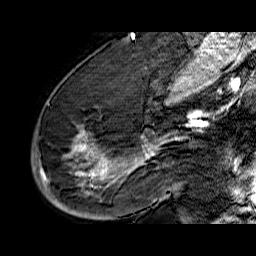
Breast MRI (dynamic contrast-enhanced), one sagittal slice; position 38 of 60 along the scan axis; dynamic contrast-enhanced series, time point 2 of 6 at this slice position (early post-contrast); 1.5 T; TE 6.5 ms, TR 32.9 ms; 4 mm slice thickness; 256 × 256 image matrix, field of view 200 × 200 mm. Female patient. From the clinical record (not read from this slice): setting: breast cancer imaged before/during neoadjuvant chemotherapy; receptor status: HR-positive, HER2-negative.
Annotated regions visible in this slice (semi-automatic segmentation, software-assisted and operator-edited):
- analysis volume of interest (the breast-tissue region the enhancement analysis was run in; not a lesion): box from (x=33, y=74) to (x=176, y=210) px
- tumour enhancement mask (voxels above the 100 % enhancement threshold inside the analysis volume of interest): (x=39, y=133)–(x=176, y=195)